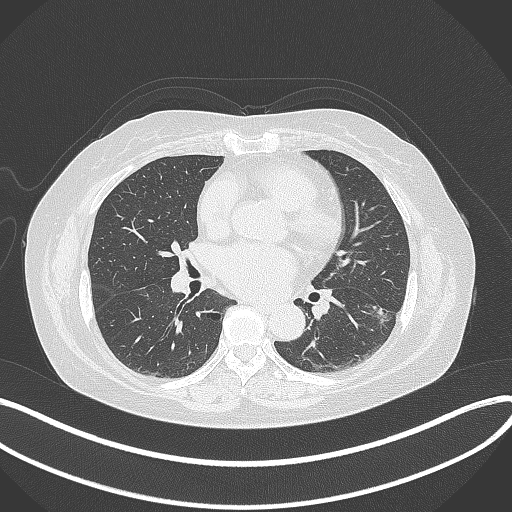
Chest CT, one axial slice; slice 177 of 373 in the series (ordered by position); 120 kVp; lung window (W 1500 / L -600 HU); 1 mm slice thickness; 512 × 512 image matrix, field of view 400 × 400 mm. Patient: female, 67 years. Case-level facts recorded for this patient, not image findings: clinical TNM (as recorded): T1c N0 M0.
Outlined on this slice (rectangle marked by the reading radiologist):
- lung tumour (recorded histology: adenocarcinoma): bounding box <363,295,395,327> (left, top, right, bottom; pixels)